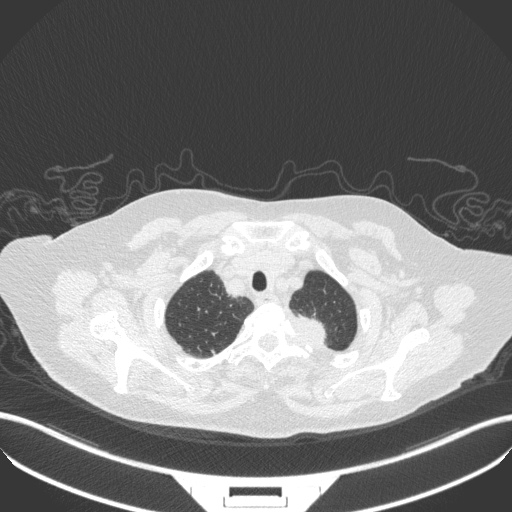
Chest CT, one axial slice. Slice 305 of 353 in the series (ordered by position). Lung window (W 1500 / L -600 HU). 512 × 512 image matrix, field of view 400 × 400 mm. Patient: female, 81 years. From the clinical record (not read from this slice): clinical TNM (as recorded): T2a N0 M0.
Structures marked on this image (bounding box drawn by a radiologist):
- lung tumour (recorded histology: adenocarcinoma): bounding box <289,307,338,356> (left, top, right, bottom; pixels)